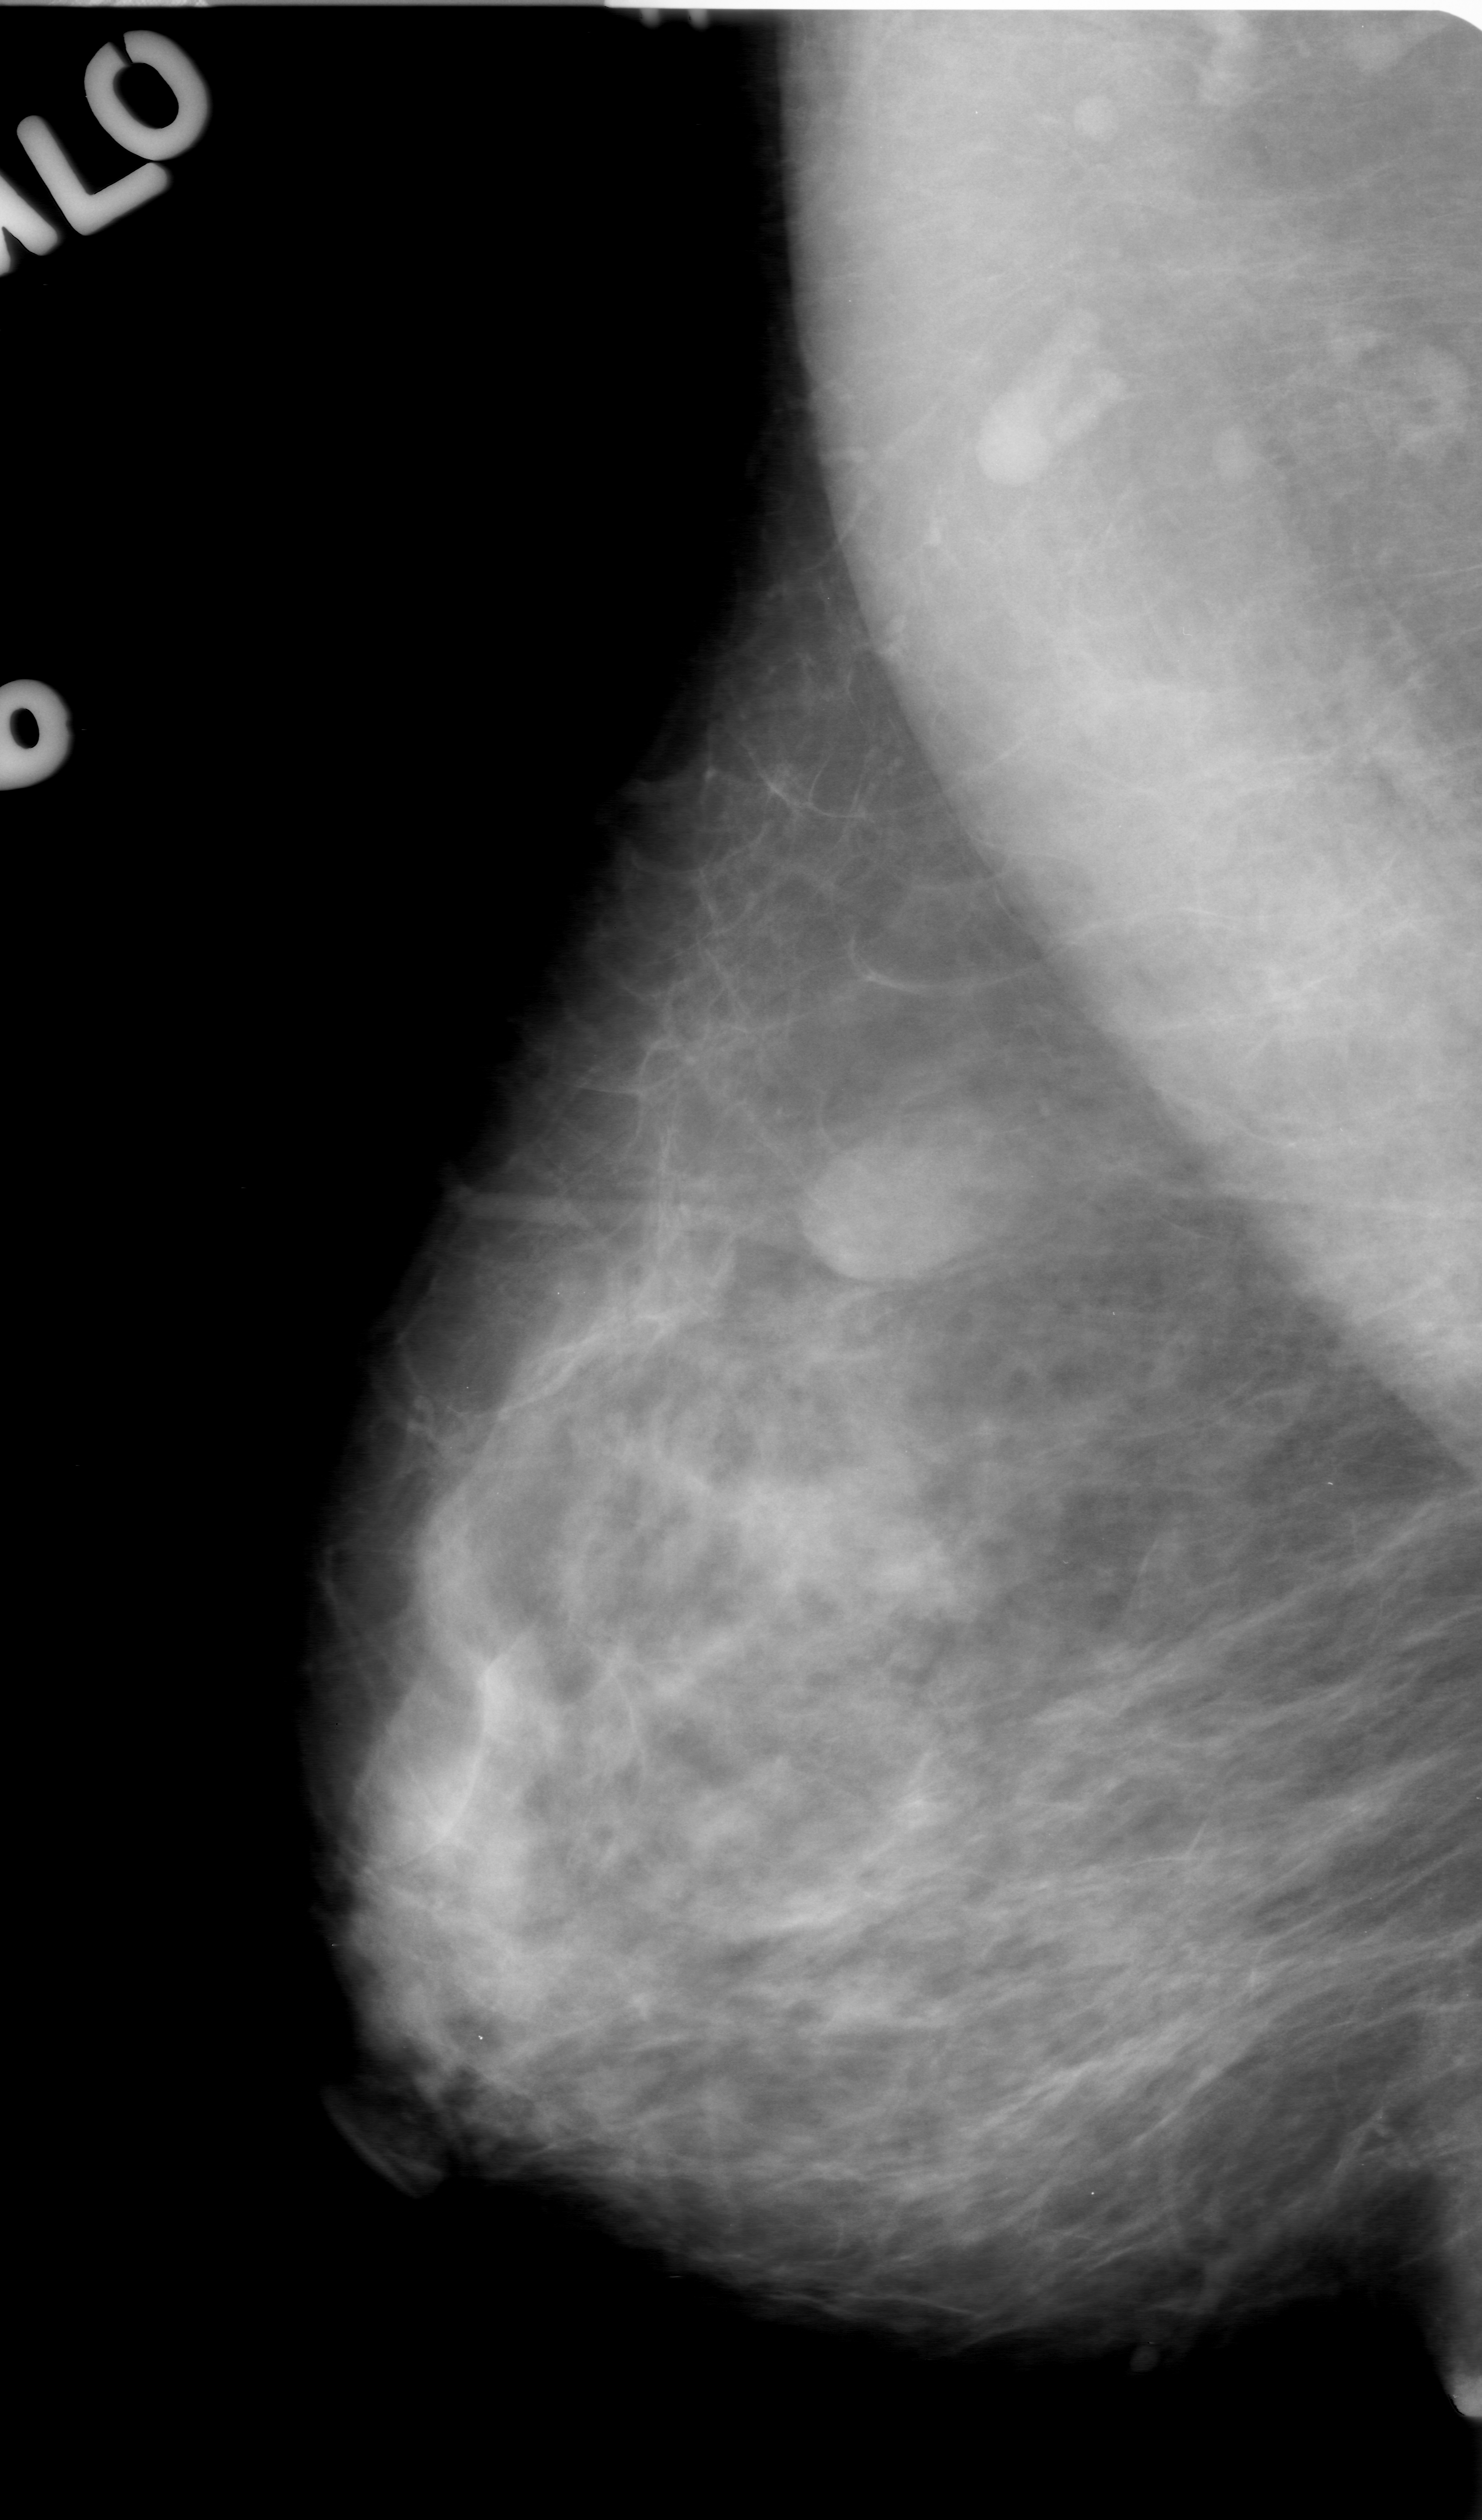
Scanned film-screen mammogram, right breast, mediolateral oblique (MLO) view, BI-RADS breast density category 3 (scale 1–4).
Mass, shape oval, margins obscured; BI-RADS assessment category 0 (incomplete: needs additional imaging); subtlety rating 4 on a 1 (subtle) to 5 (obvious) scale; pathology result (as recorded, not read from the image): benign.